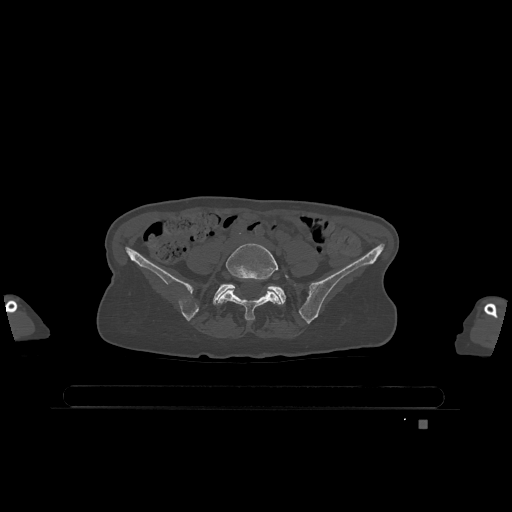
CT including the spine, one axial slice. Slice 227 of 1317 in the series (ordered by position). Bone window (W 1800 / L 400 HU). 0.5 mm slice thickness. 512 × 512 image matrix, field of view 500 × 500 mm. Patient: female, 74 years. From the clinical record (not read from this slice): primary cancer: lung.
Structures marked on this image (semi-automatically segmented with operator editing):
- L5 vertebra: box from (x=217, y=243) to (x=289, y=321) px